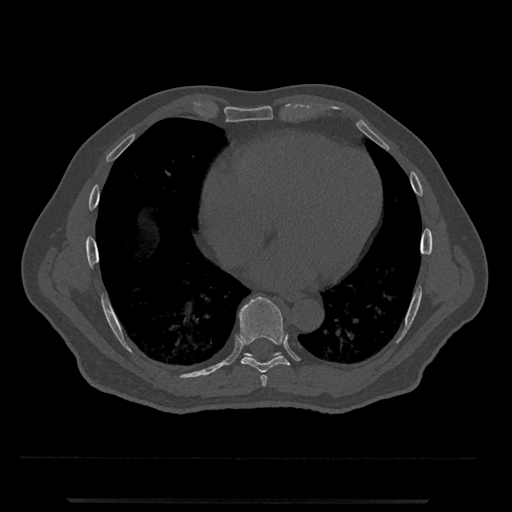
CT including the spine, one axial slice. Slice 619 of 797 in the series (ordered by position). Reconstruction kernel Br40s/3. 120 kVp. Bone window (W 1800 / L 400 HU). 0.5 mm slice thickness. 512 × 512 image matrix. Male patient, age 63 years. From the clinical record (not read from this slice): primary cancer: prostate.
Annotated regions visible in this slice (semi-automatically segmented with operator editing):
- T7 vertebra: box from (x=260, y=375) to (x=267, y=387) px
- T8 vertebra: (x=238, y=296)–(x=290, y=373)
- T9 vertebra: (x=244, y=352)–(x=281, y=359)